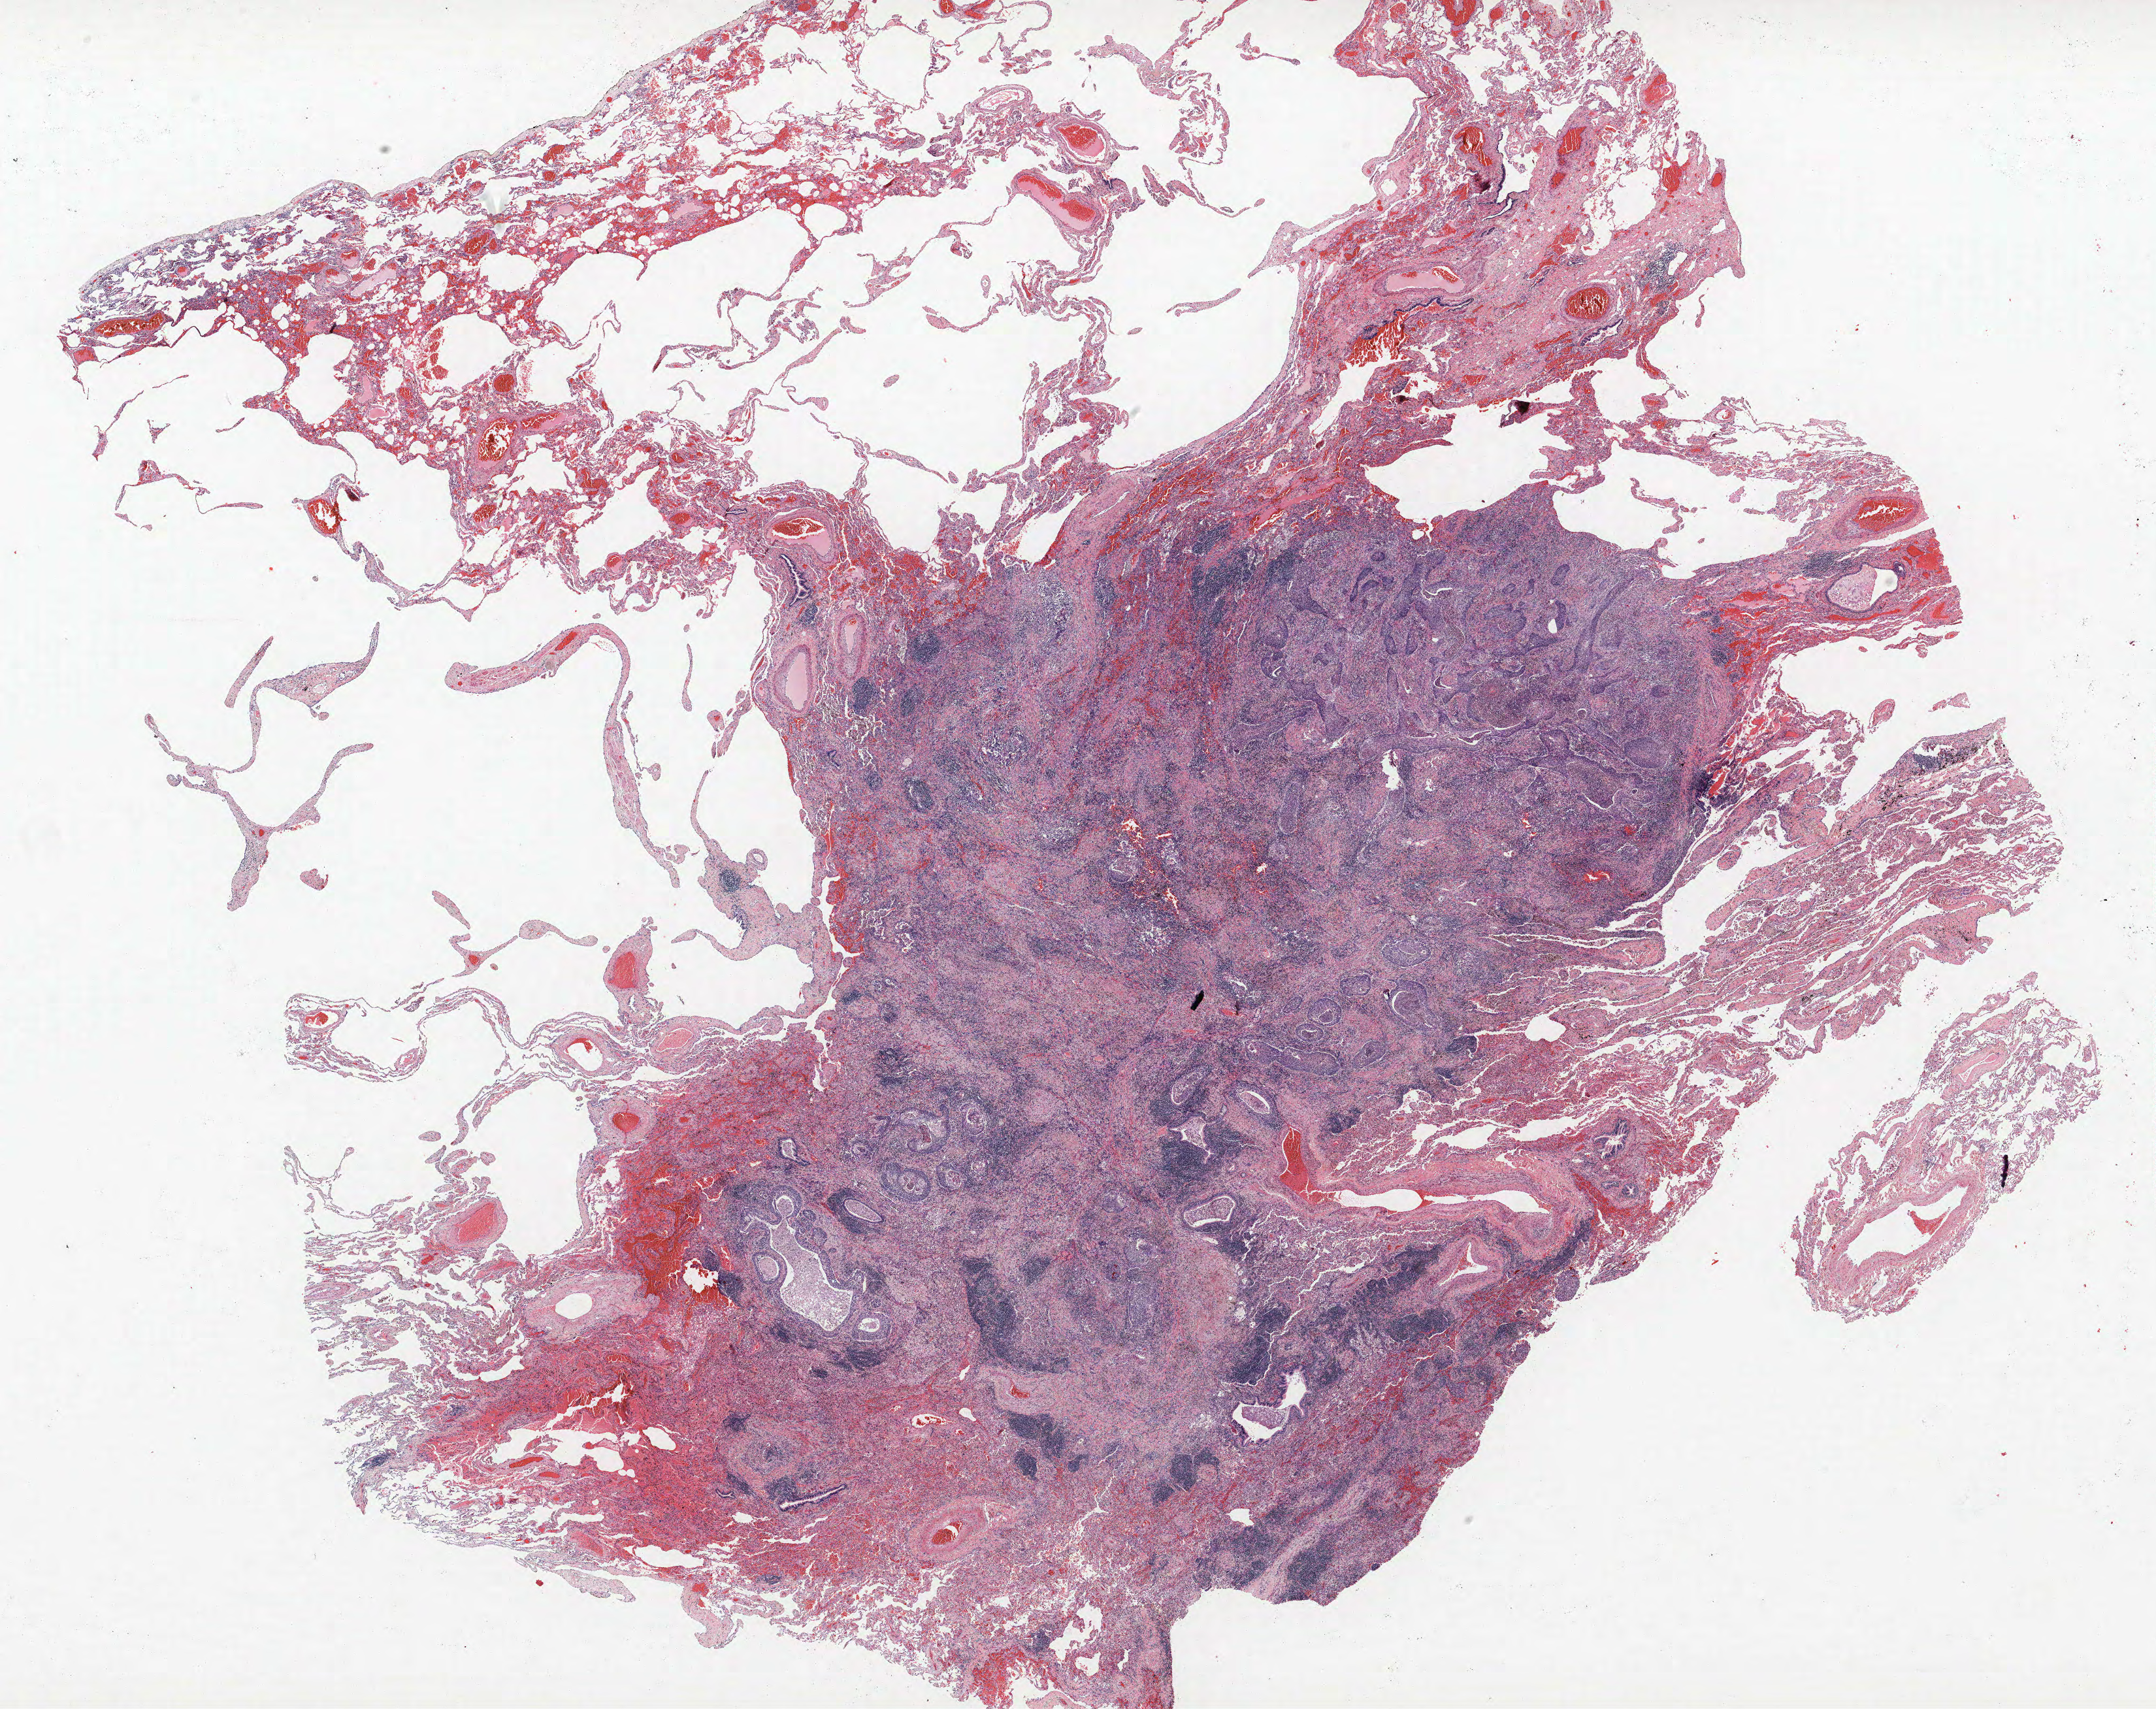
H&E whole-slide image — whole scanned area (about 26.4 x 20.9 mm, slide scanned at 40x) shown as a low-resolution overview; FFPE section; lung. Female, age 64 at enrolment. Current smoker at enrolment. Grade: moderately differentiated (G2).
- stage (AJCC 6th edition): IA
- tumour size (pathology): 15 mm
- participant's lung-cancer diagnosis: Squamous cell carcinoma, NOS
- primary tumour location (clinical record): left upper lobe